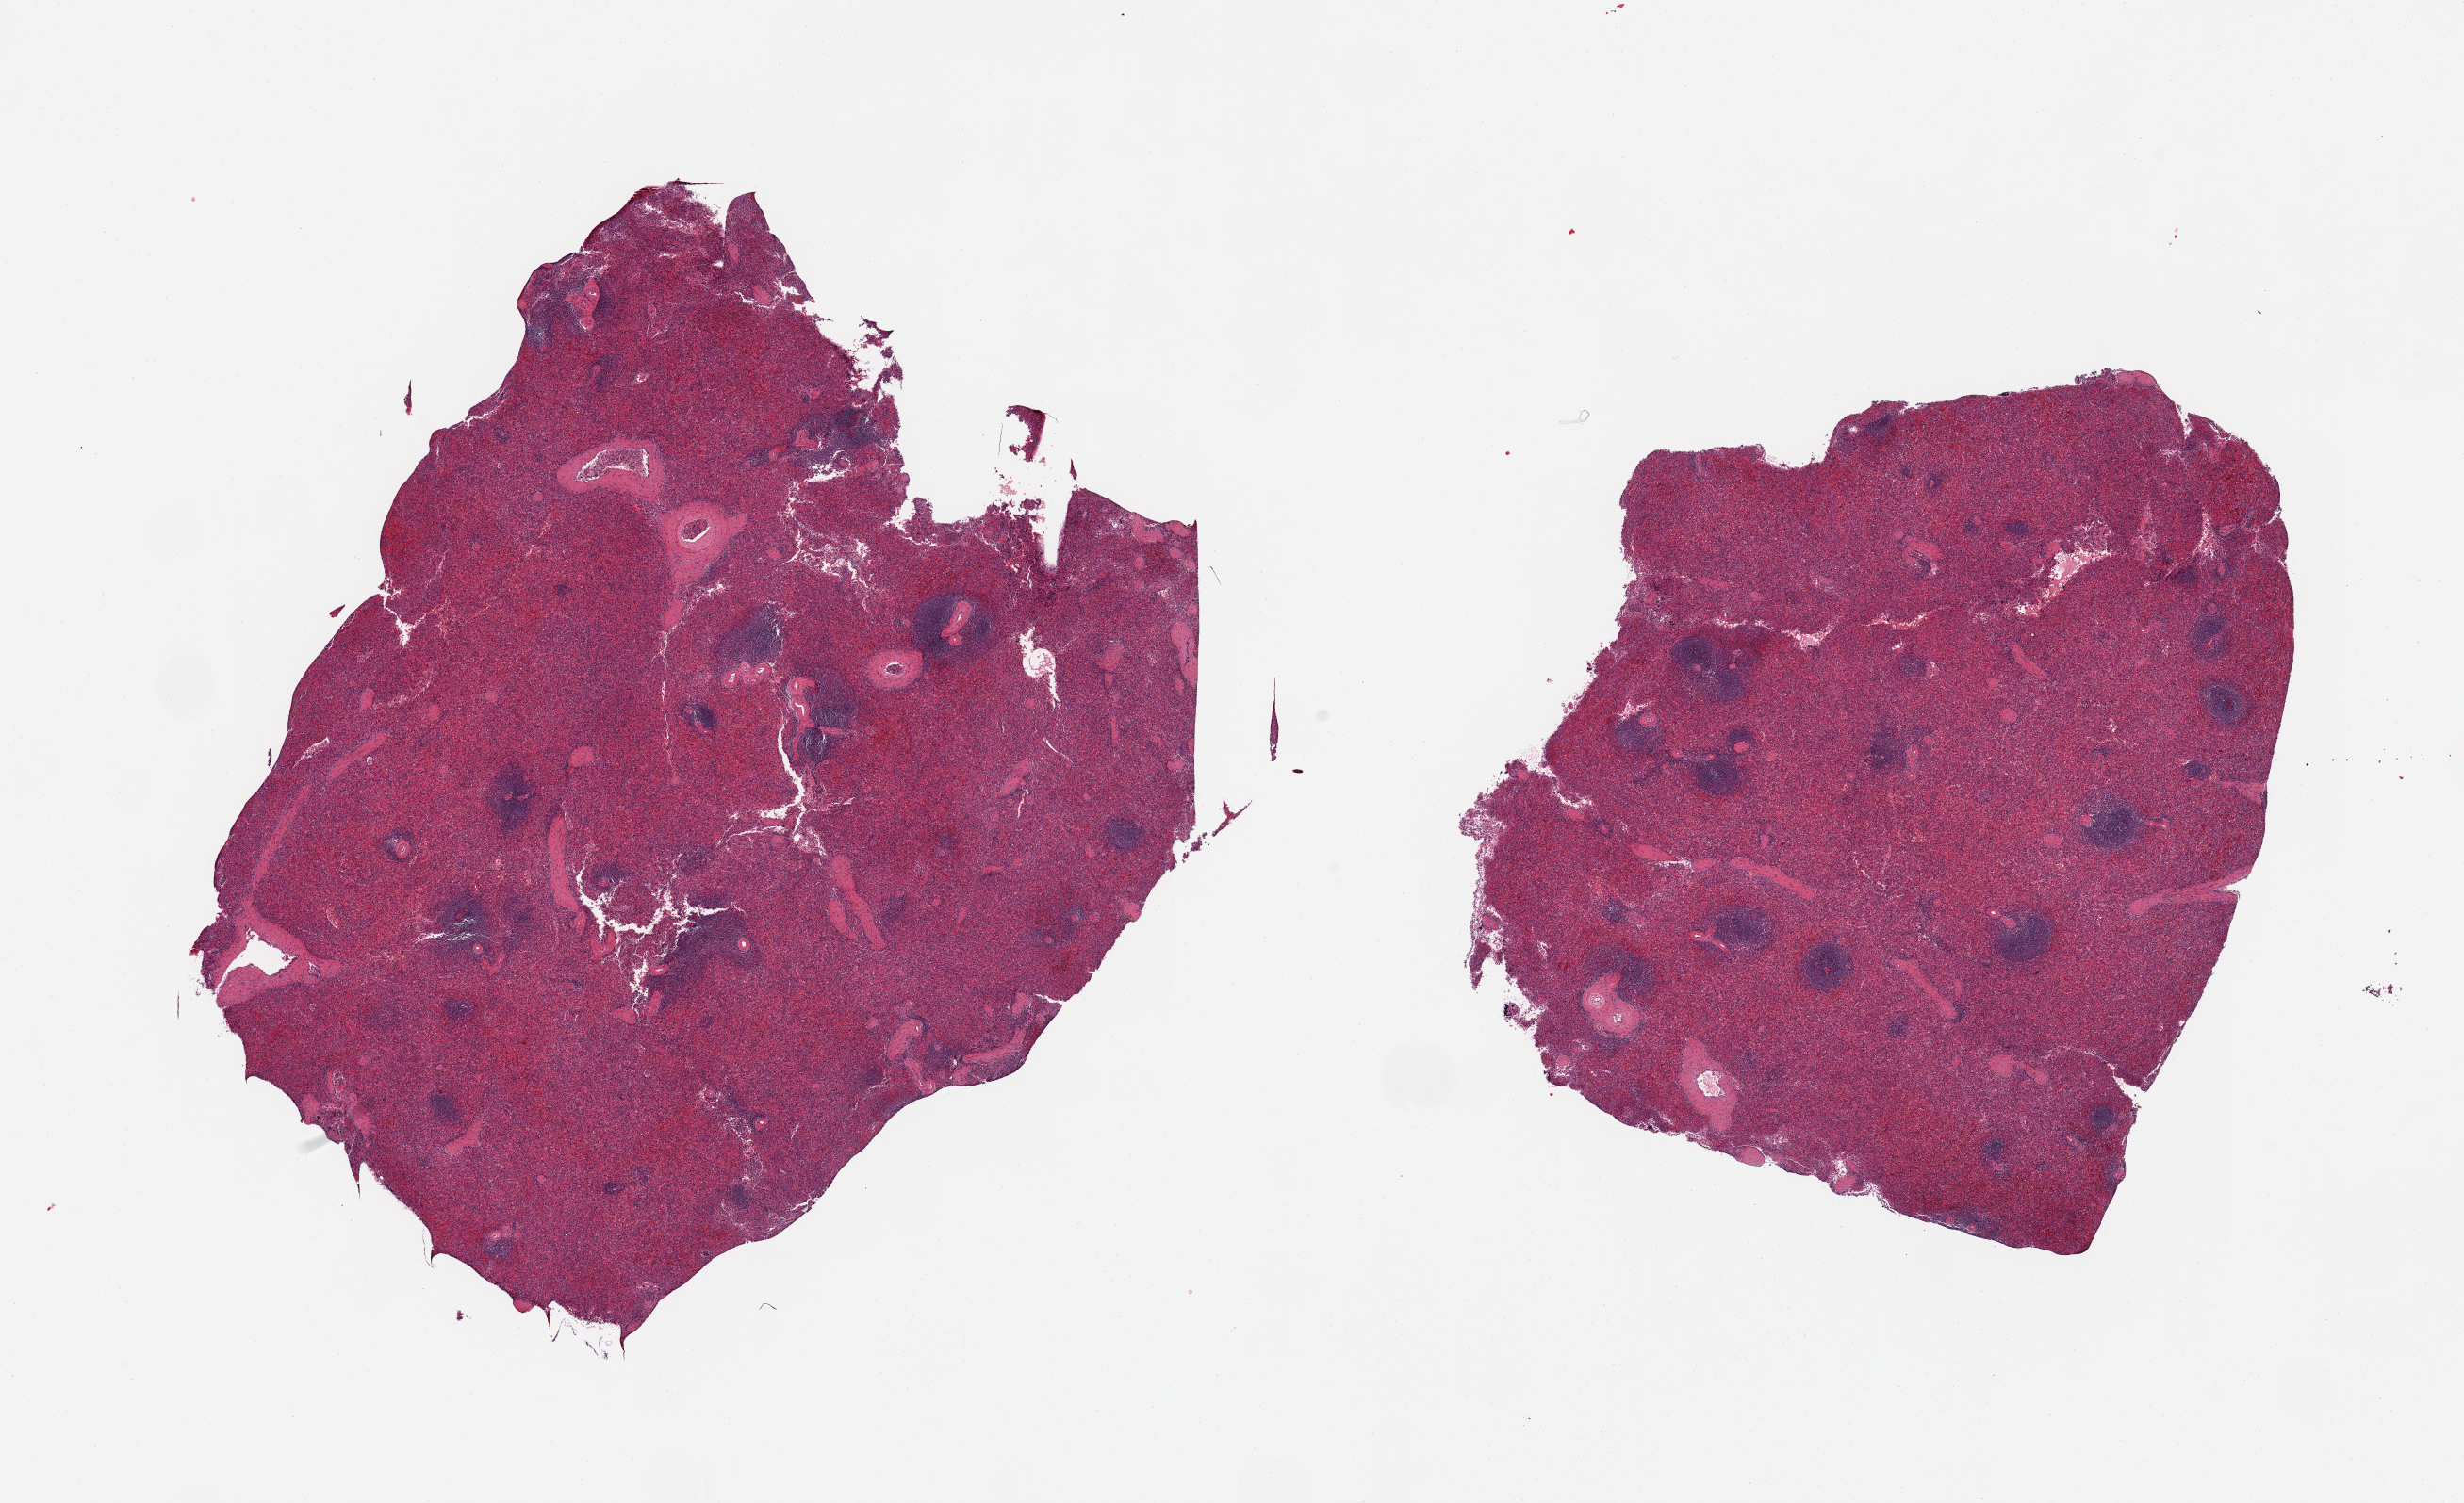
H&E whole-slide image — a low-resolution overview of the entire scanned area, about 20.7 x 12.6 mm; PAXgene-fixed paraffin-embedded (PFPE) section; target tissue: spleen; tissue donor sample. Donor: male.
Reviewer comment on this tissue sample: 2 pieces; congestion.